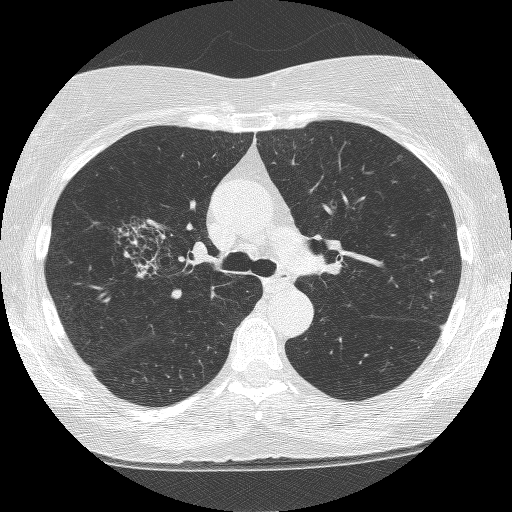
Axial slice from a low-dose chest CT screening exam, second annual screen, lung window (W 1500 / L -600 HU), 1.25 mm slice thickness, 120 kVp, 512 × 512 image matrix. Female, age 64 years at enrolment.
Expert-annotated lung lesion, bounding box <115,204,209,292> (left, top, right, bottom; pixels). The screening reader recorded 4 non-calcified nodules or masses ≥4 mm on this exam; which of them this box marks is not recorded. Official screen result: positive, other. Later outcome: lung cancer diagnosed 381 days after this screen (after the third annual screen) — adenocarcinoma, NOS, right upper lobe, right middle lobe, right hilum, stage IV (AJCC 6th edition), 85 mm at pathology.